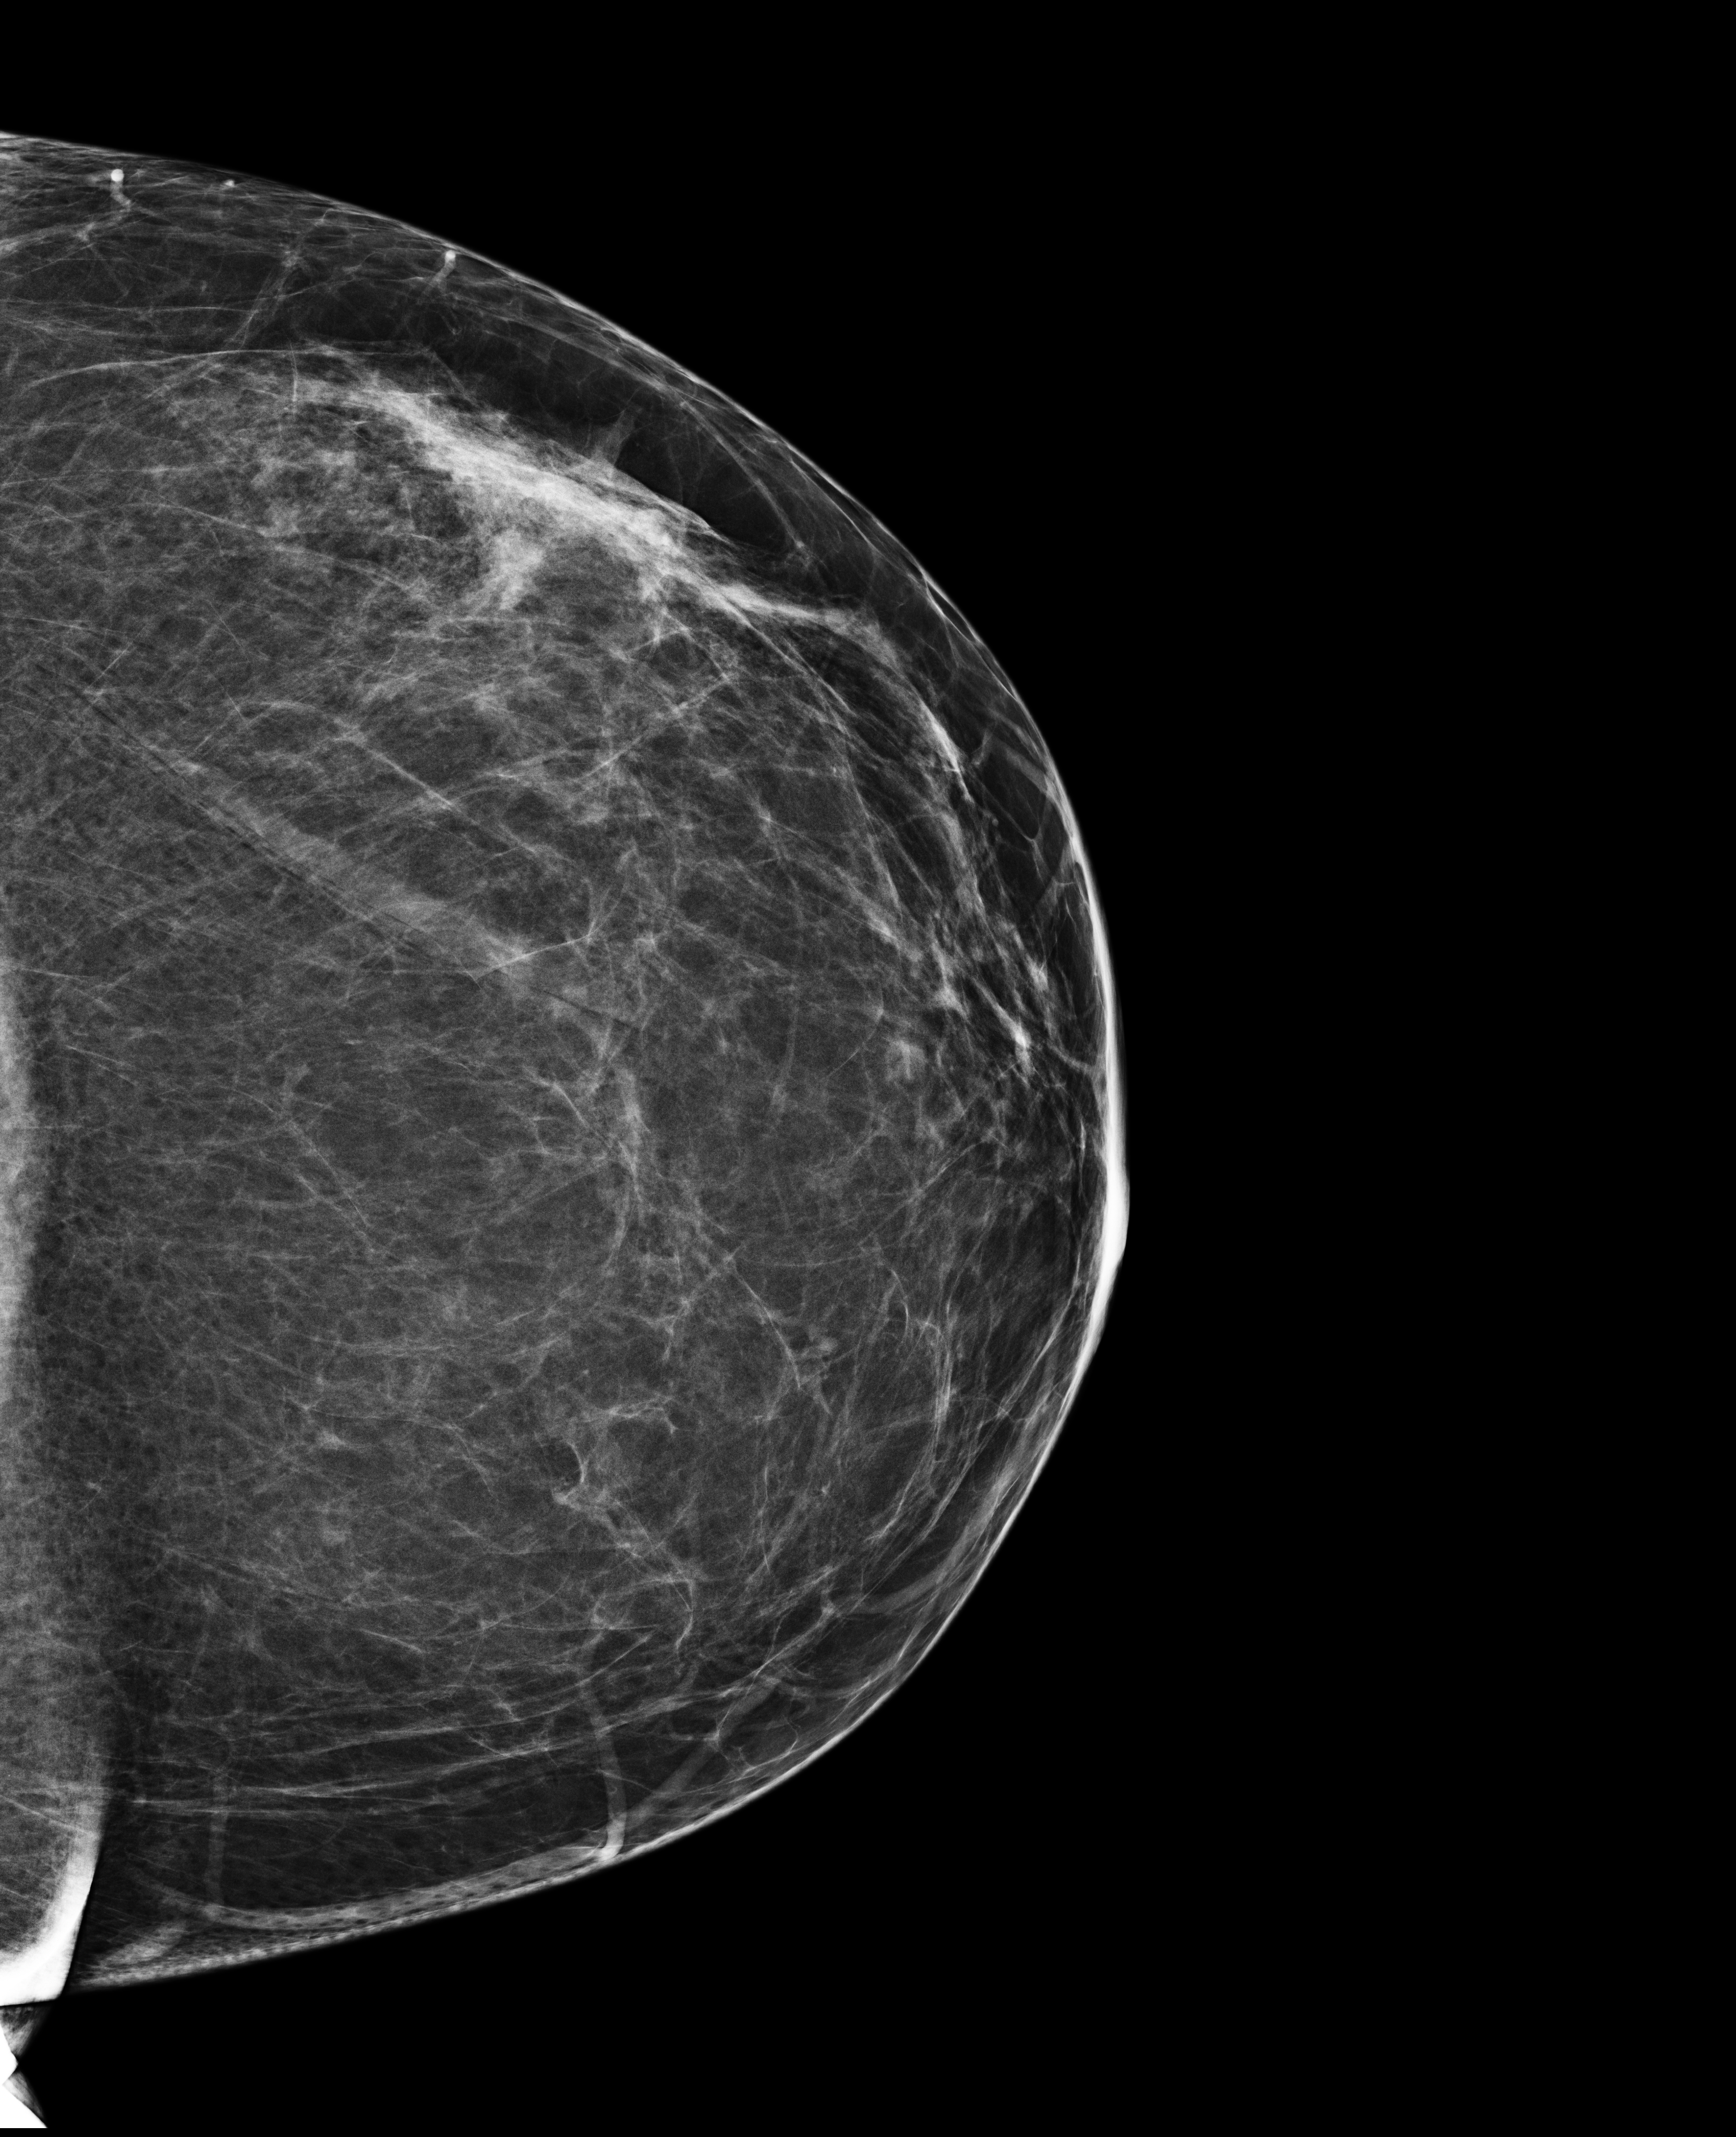
Digital mammogram (FFDM); left breast; craniocaudal (CC) view; screening examination; compressed breast thickness 71 mm. Female patient, age 52 years.
BI-RADS breast density category at the screening exam (both breasts, scale 1–4): 2. Final BI-RADS assessment for this screening round (tomosynthesis exam, both breasts): category 2. Recall: no recall after this screen.